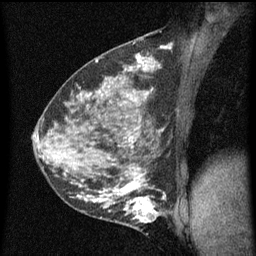
Breast MRI (dynamic contrast-enhanced), one sagittal slice. Slice 31 of 60 in the series (ordered by position). Dynamic contrast-enhanced series, image 2 of 5 at this slice position (ordered by acquisition). 1.5 T. TE 4.2 ms, TR 8 ms. 256 × 256 image matrix, field of view 180 × 180 mm. Patient: female, 35 years.
Outlined on this slice (semi-automatic segmentation, software-assisted and operator-edited):
- analysis volume of interest (the breast-tissue region the enhancement analysis was run in; not a lesion): box from (x=118, y=190) to (x=165, y=229) px
- tumour enhancement mask (voxels above the 70 % enhancement threshold inside the analysis volume of interest): (x=118, y=190)–(x=165, y=223)